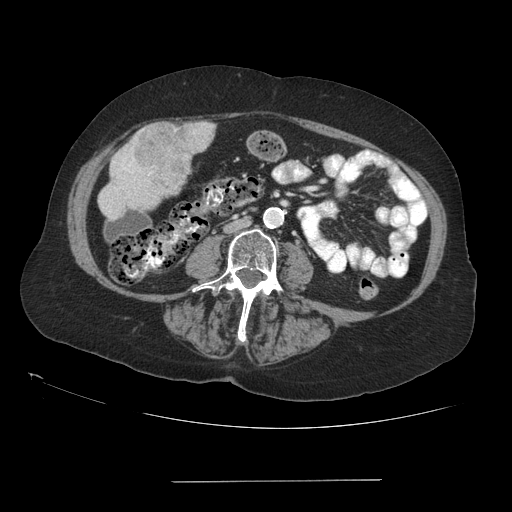
Contrast-enhanced abdominal CT (liver protocol), one axial slice; position 18 of 89 along the scan axis; 140 kVp; soft-tissue window (W 400 / L 40 HU); 2.5 mm slice thickness; 512 × 512 image matrix. From the clinical record (not read from this slice): diagnosis: hepatocellular carcinoma (patient treated with transarterial chemoembolisation; whether this scan precedes or follows treatment is not stated here); TNM stage (as recorded): Stage-IVA; Child-Pugh class: A.
Annotated regions visible in this slice (semi-automatic segmentation, software-assisted and operator-edited):
- liver parenchyma outside the tumour (the mass and vessels are separate outlines, so this box may not span the whole liver): bounding box [x1, y1, x2, y2] px = [98, 122, 212, 220]
- mass: [131, 120, 216, 191]